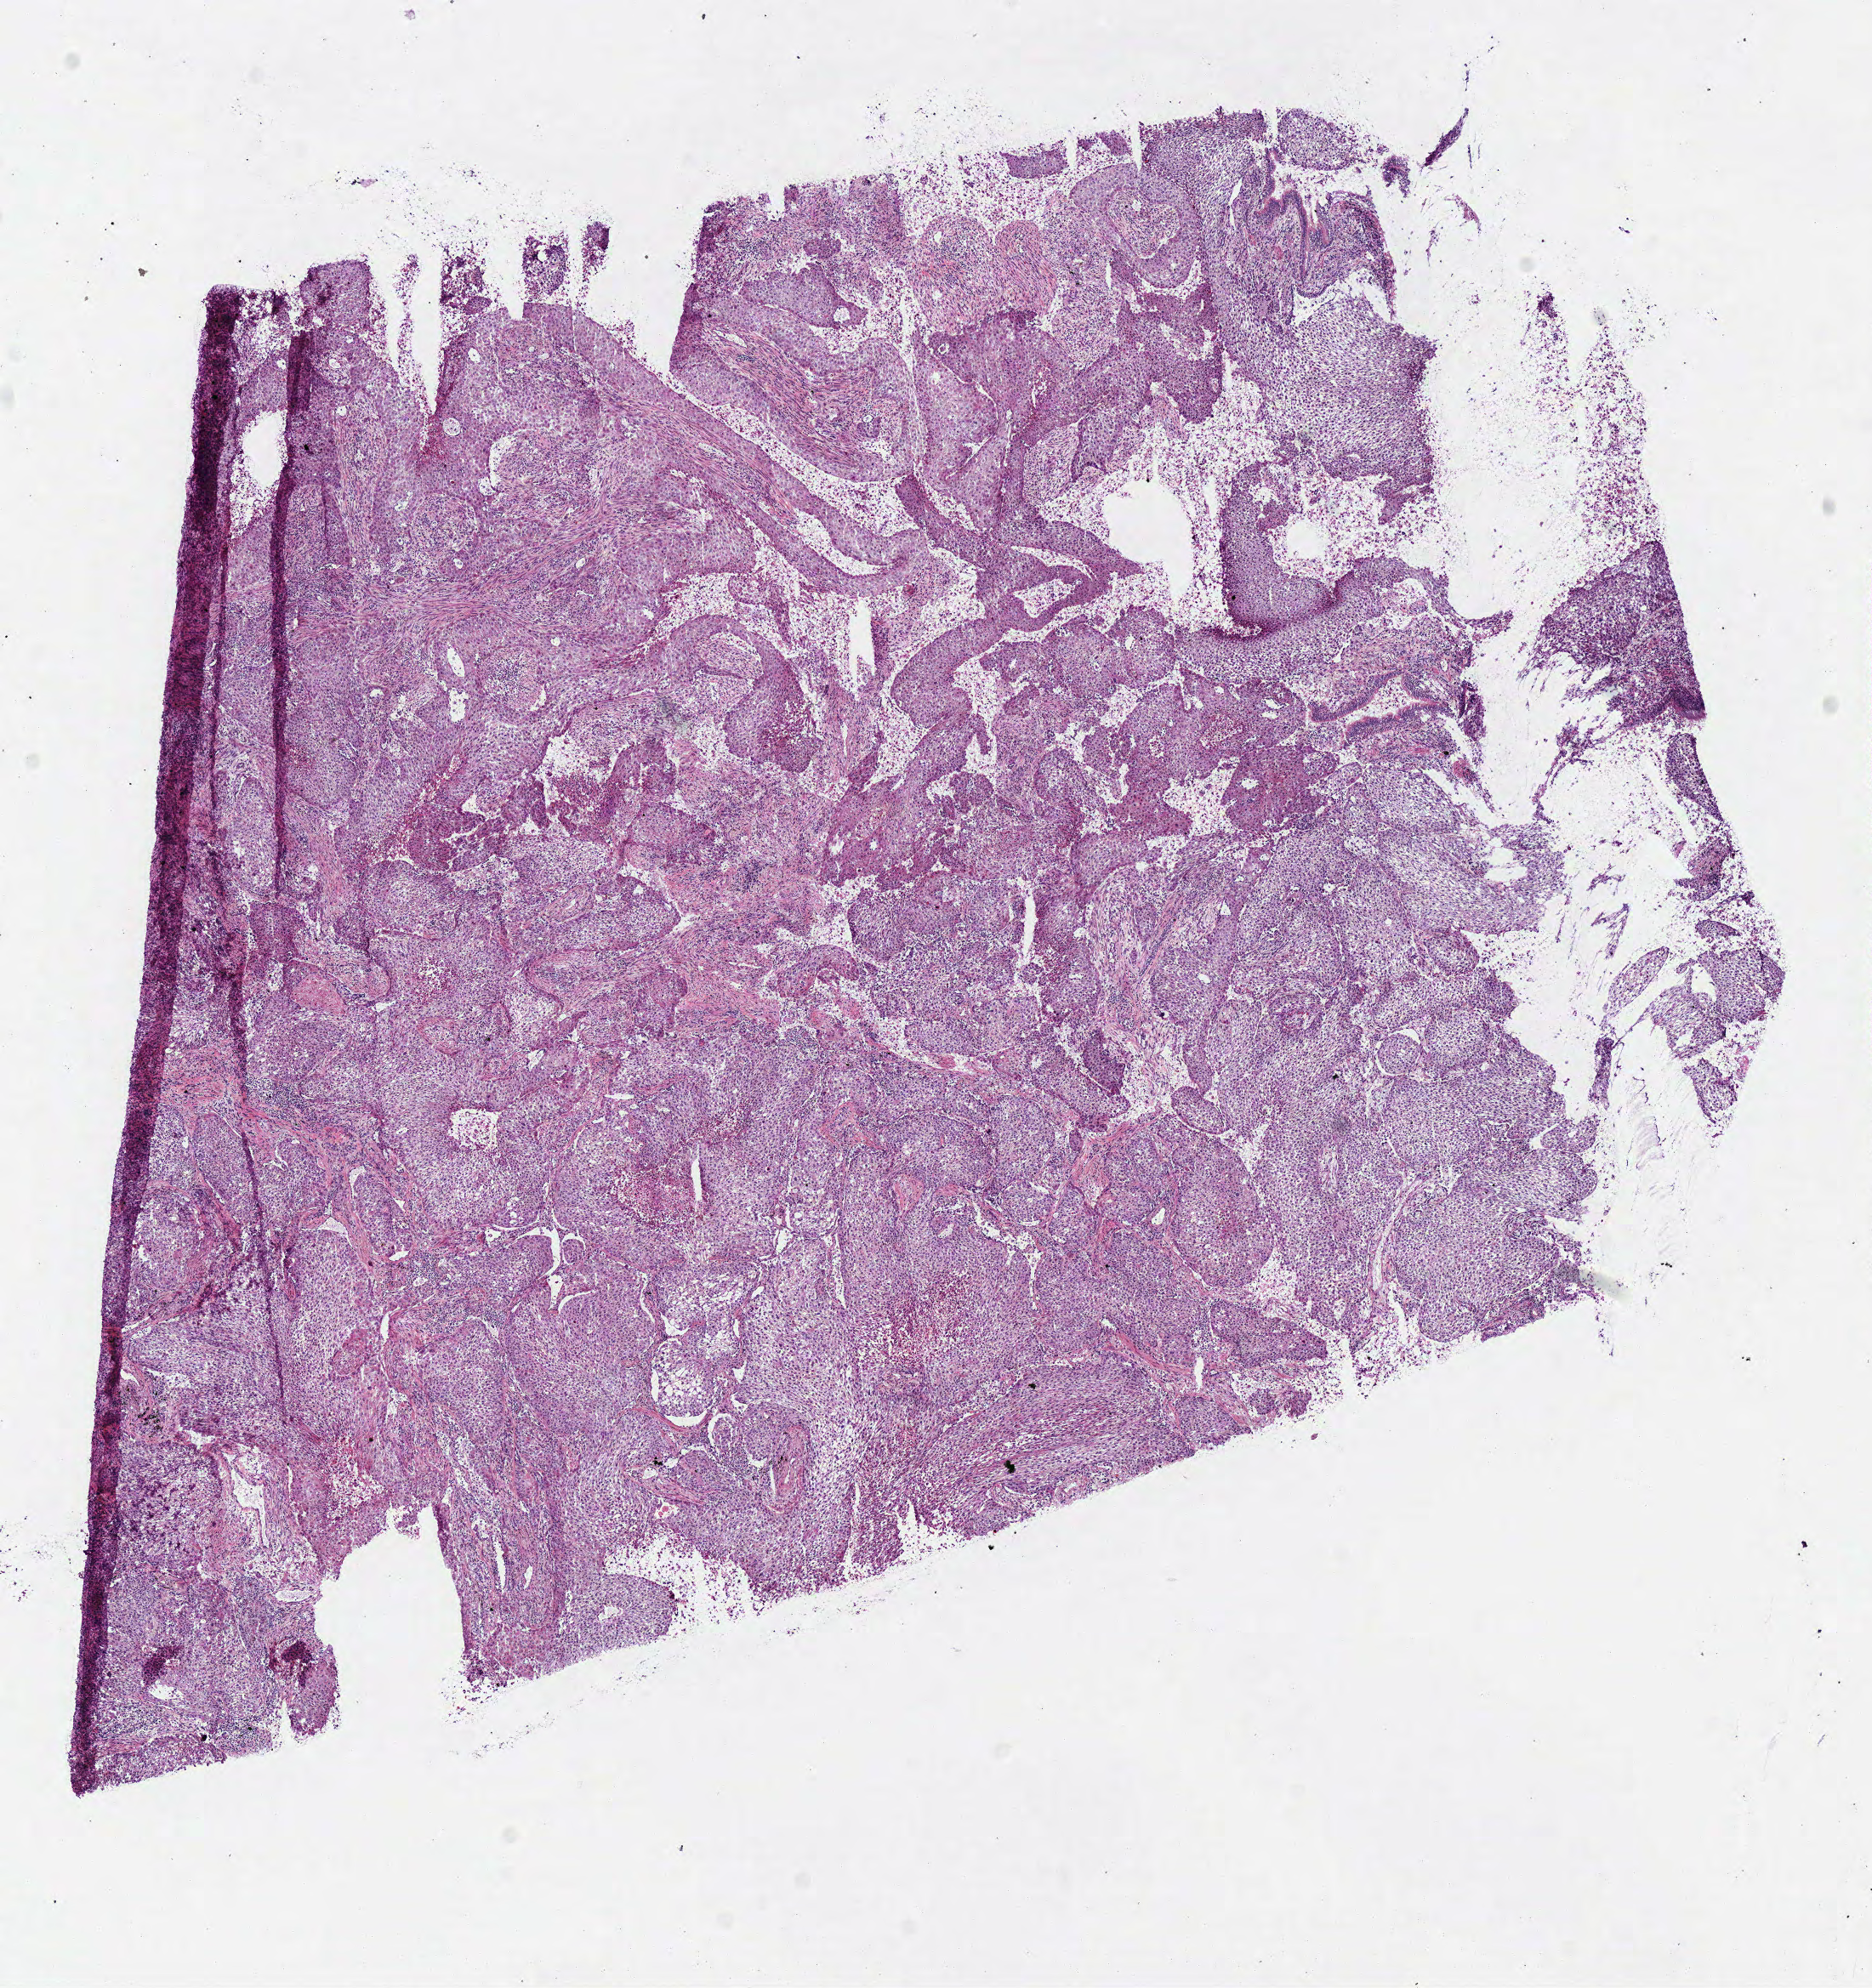
H&E whole-slide image, shown as a low-resolution overview of the whole scanned area (about 8.7 x 9.2 mm, acquisition: 40x scan); frozen section; primary tumour sample from the lung. Patient: male, age at initial diagnosis 74 years. Composition of this section per pathologist review: tumour cells 98%, tumour nuclei 85%, normal cells 0%, stromal cells 0%, necrosis 2%.
TNM: T3 N1 M0. Histologic diagnosis: Squamous cell carcinoma, NOS (lower lobe, lung). Laterality: right. AJCC pathologic stage: IIIA (6th edition).